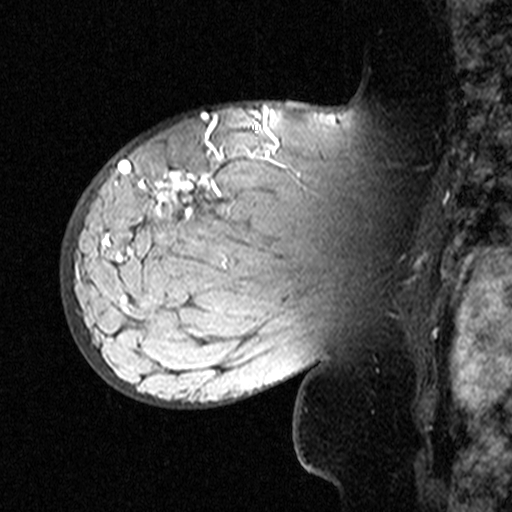
Breast MRI (dynamic contrast-enhanced), one sagittal slice; position 31 of 44 along the scan axis; dynamic contrast-enhanced study with each time point stored as its own series, time point 2 of 3 at this slice position (early post-contrast, ordered by acquisition time); 1.5 T; TE 4.5 ms, TR 11 ms; 3 mm slice thickness; 512 × 512 image matrix, field of view 200 × 200 mm. Female patient, age 53 years. From the clinical record (not read from this slice): setting: breast cancer imaged before/during neoadjuvant chemotherapy; receptor status: HR-positive, HER2-negative.
Annotated regions visible in this slice (semi-automatically segmented with operator editing):
- analysis volume of interest (the breast-tissue region the enhancement analysis was run in; not a lesion): bounding box (x1, y1, x2, y2) in pixels: (76, 140, 311, 353)
- tumour enhancement mask (voxels above the 90 % enhancement threshold inside the analysis volume of interest): (103, 146, 223, 260)